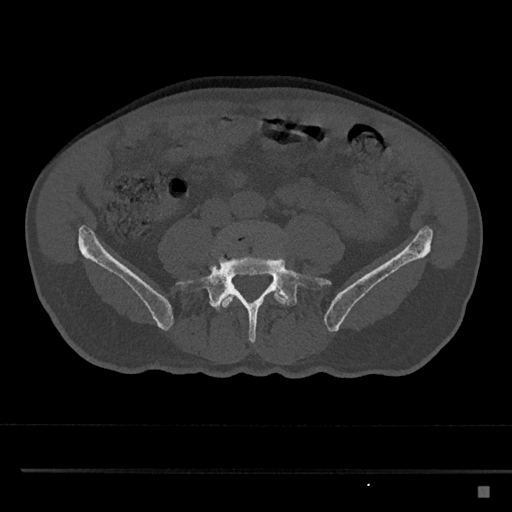
CT including the spine, one axial slice; slice 598 of 797 in the series (ordered by position); bone window (W 1800 / L 400 HU); 0.5 mm slice thickness; 512 × 512 image matrix. Patient: male, 59 years. From the clinical record (not read from this slice): primary cancer: prostate.
Structures marked on this image (semi-automatically segmented with operator editing):
- L4 vertebra: box from (x=216, y=225) to (x=289, y=311) px
- L5 vertebra: (x=176, y=244)–(x=331, y=343)